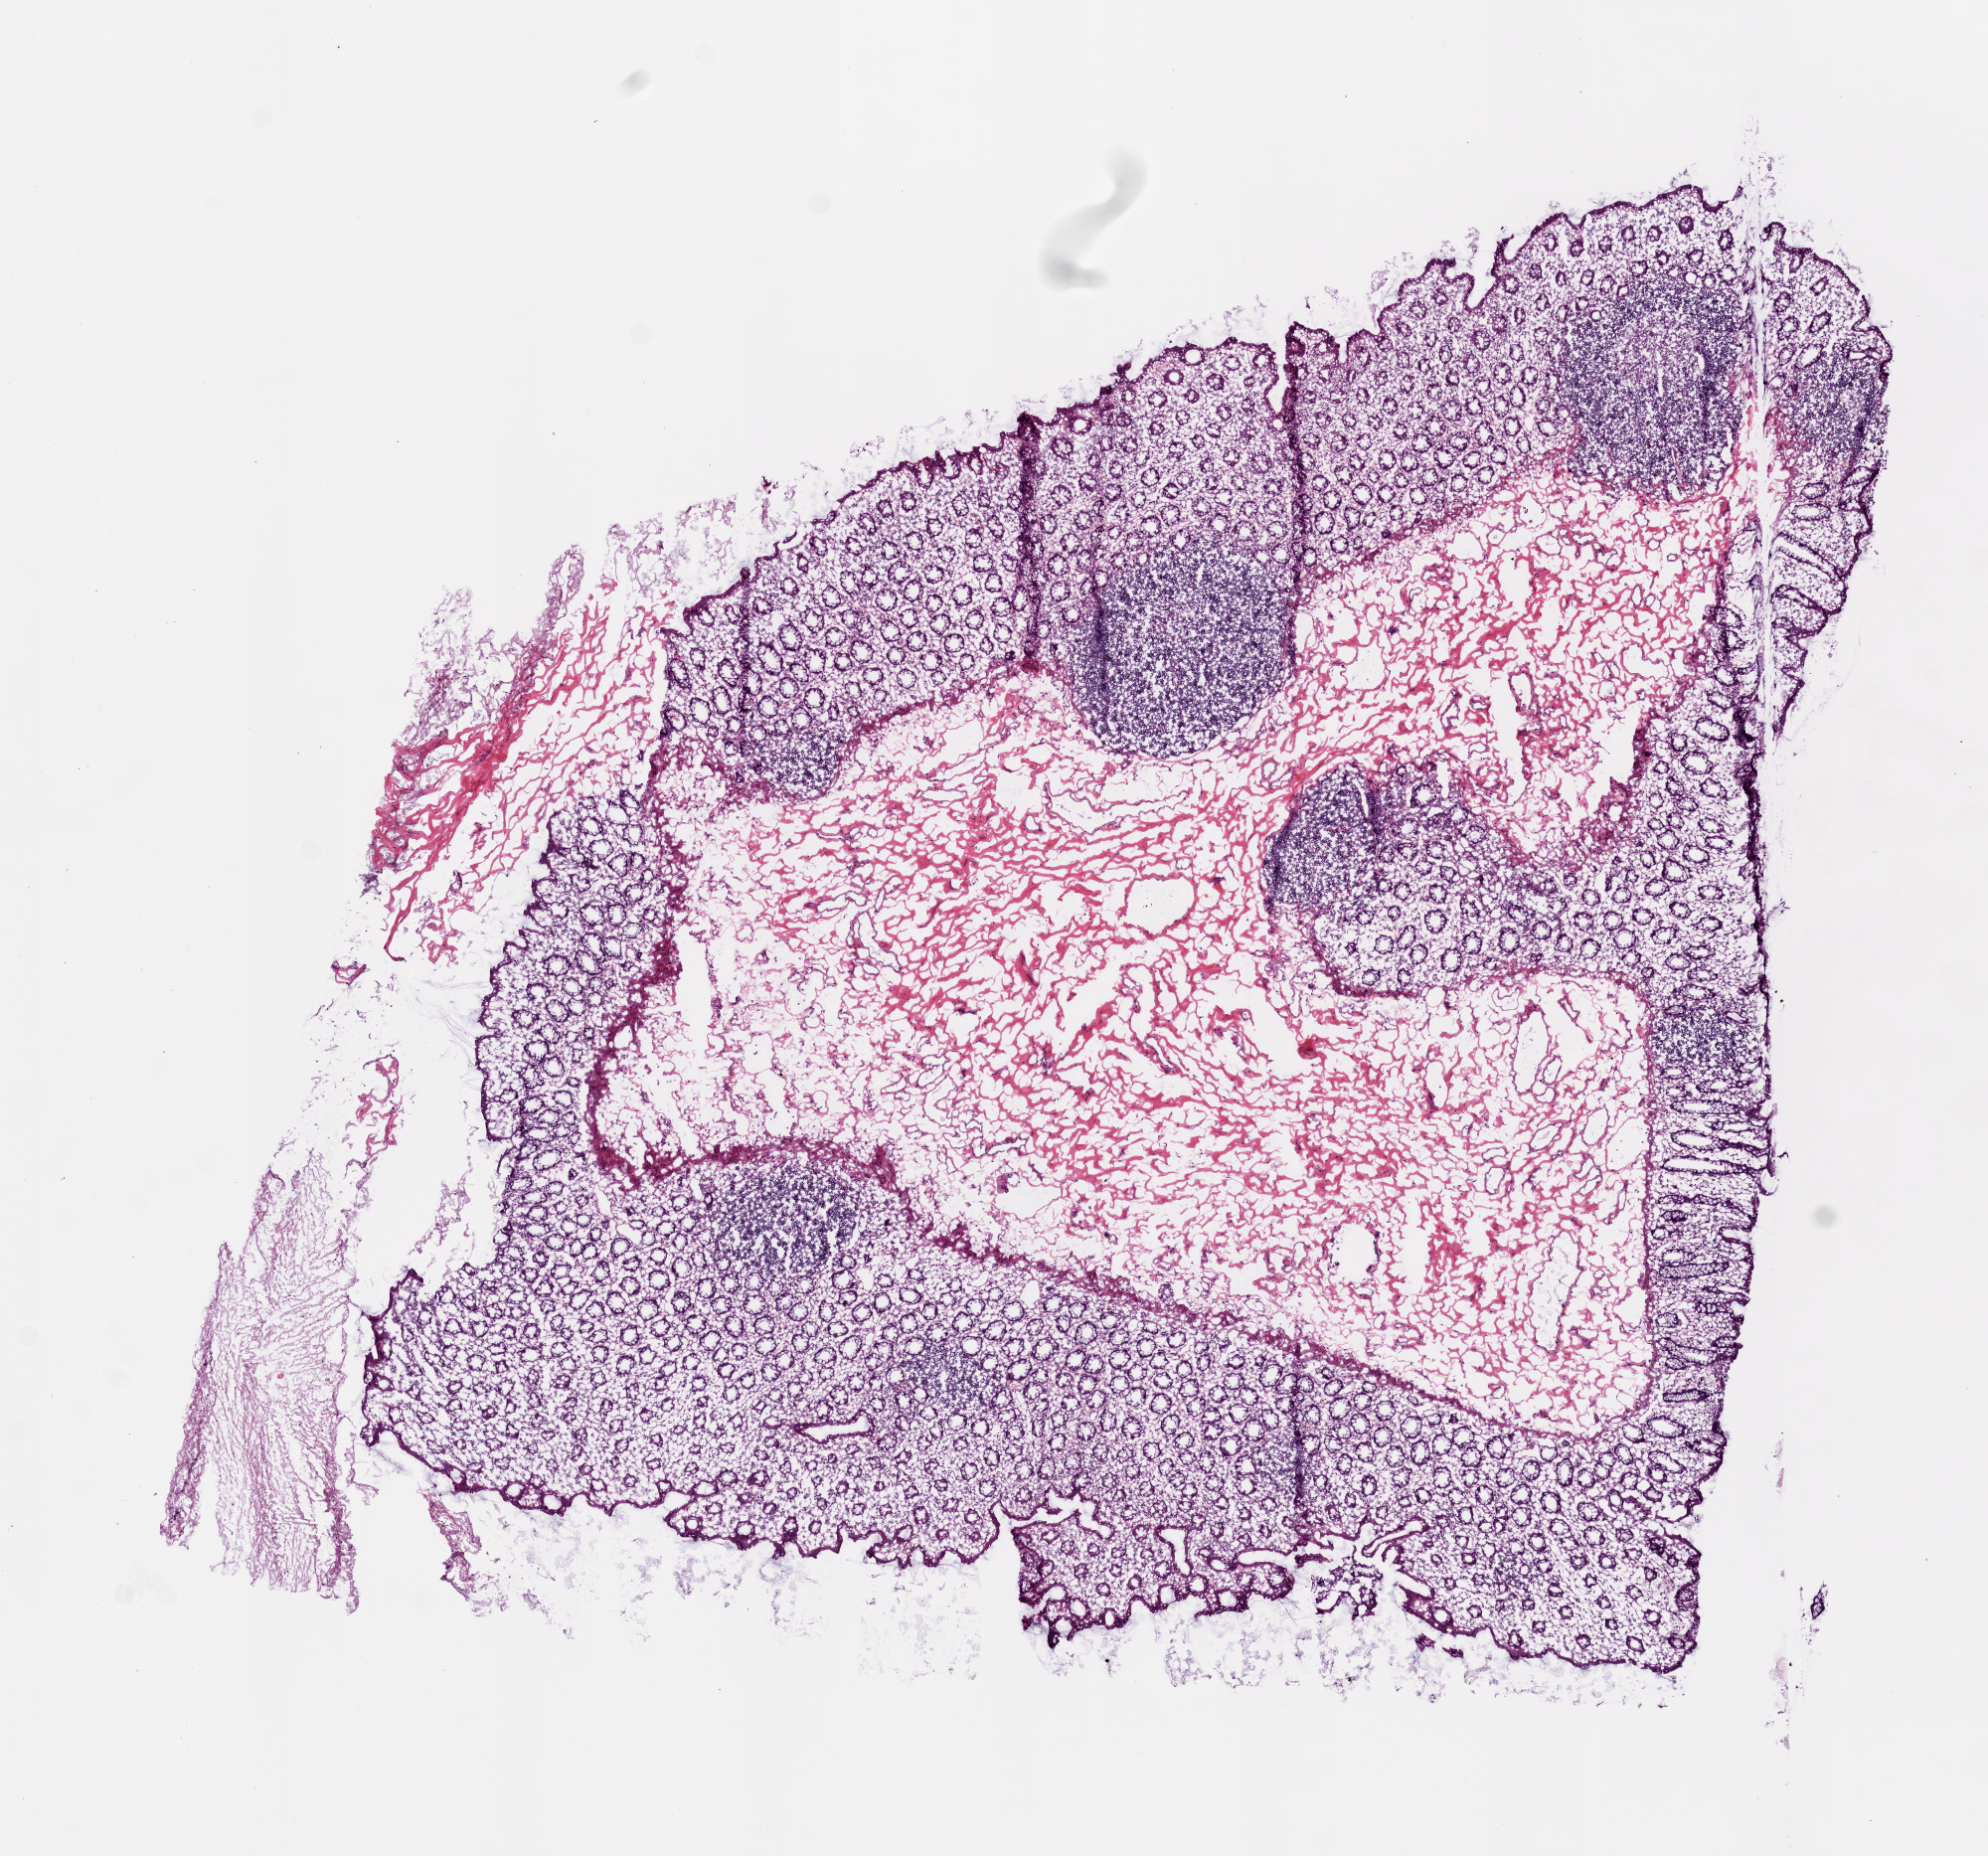
H&E-stained whole-slide image — a low-resolution overview of the entire scanned area, about 8.0 x 7.5 mm (slide scanned at 20x); frozen section from the top of the tissue portion; colon, solid tissue normal (non-tumour tissue) sample. Male patient; age at initial diagnosis 65 years.
This section: solid tissue normal sample (biorepository sample class). Patient diagnosis: Adenocarcinoma, NOS.